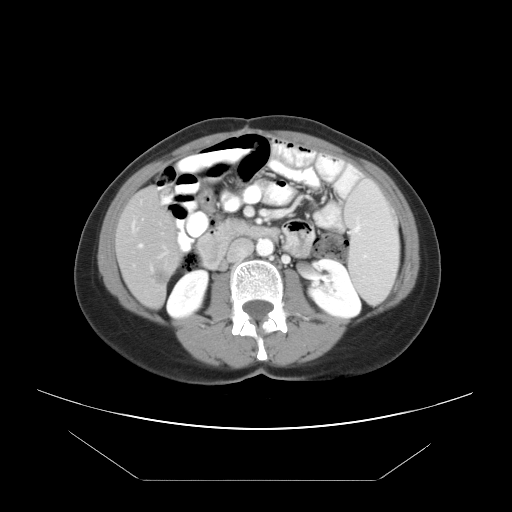
Contrast-enhanced abdominal CT, one axial slice; slice 14 of 45 in the series (ordered by position); reconstruction kernel STANDARD; soft-tissue window (W 400 / L 40 HU); 5 mm slice thickness; 512 × 512 image matrix, field of view 405 × 405 mm. Female patient, age 52 years. From the clinical record (not read from this slice): diagnosis: colorectal cancer liver metastases, imaged before liver resection; multiple liver metastases: yes.
Structures marked on this image (manually delineated by an expert):
- hepatic veins: bounding box (x1, y1, x2, y2) in pixels: (139, 244, 153, 270)
- liver: (116, 189, 179, 307)
- planned liver remnant (the part of the liver to remain after resection): (117, 189, 176, 244)
- portal vein (with intrahepatic branches): (142, 219, 168, 258)
- liver metastasis: (155, 270, 168, 286)